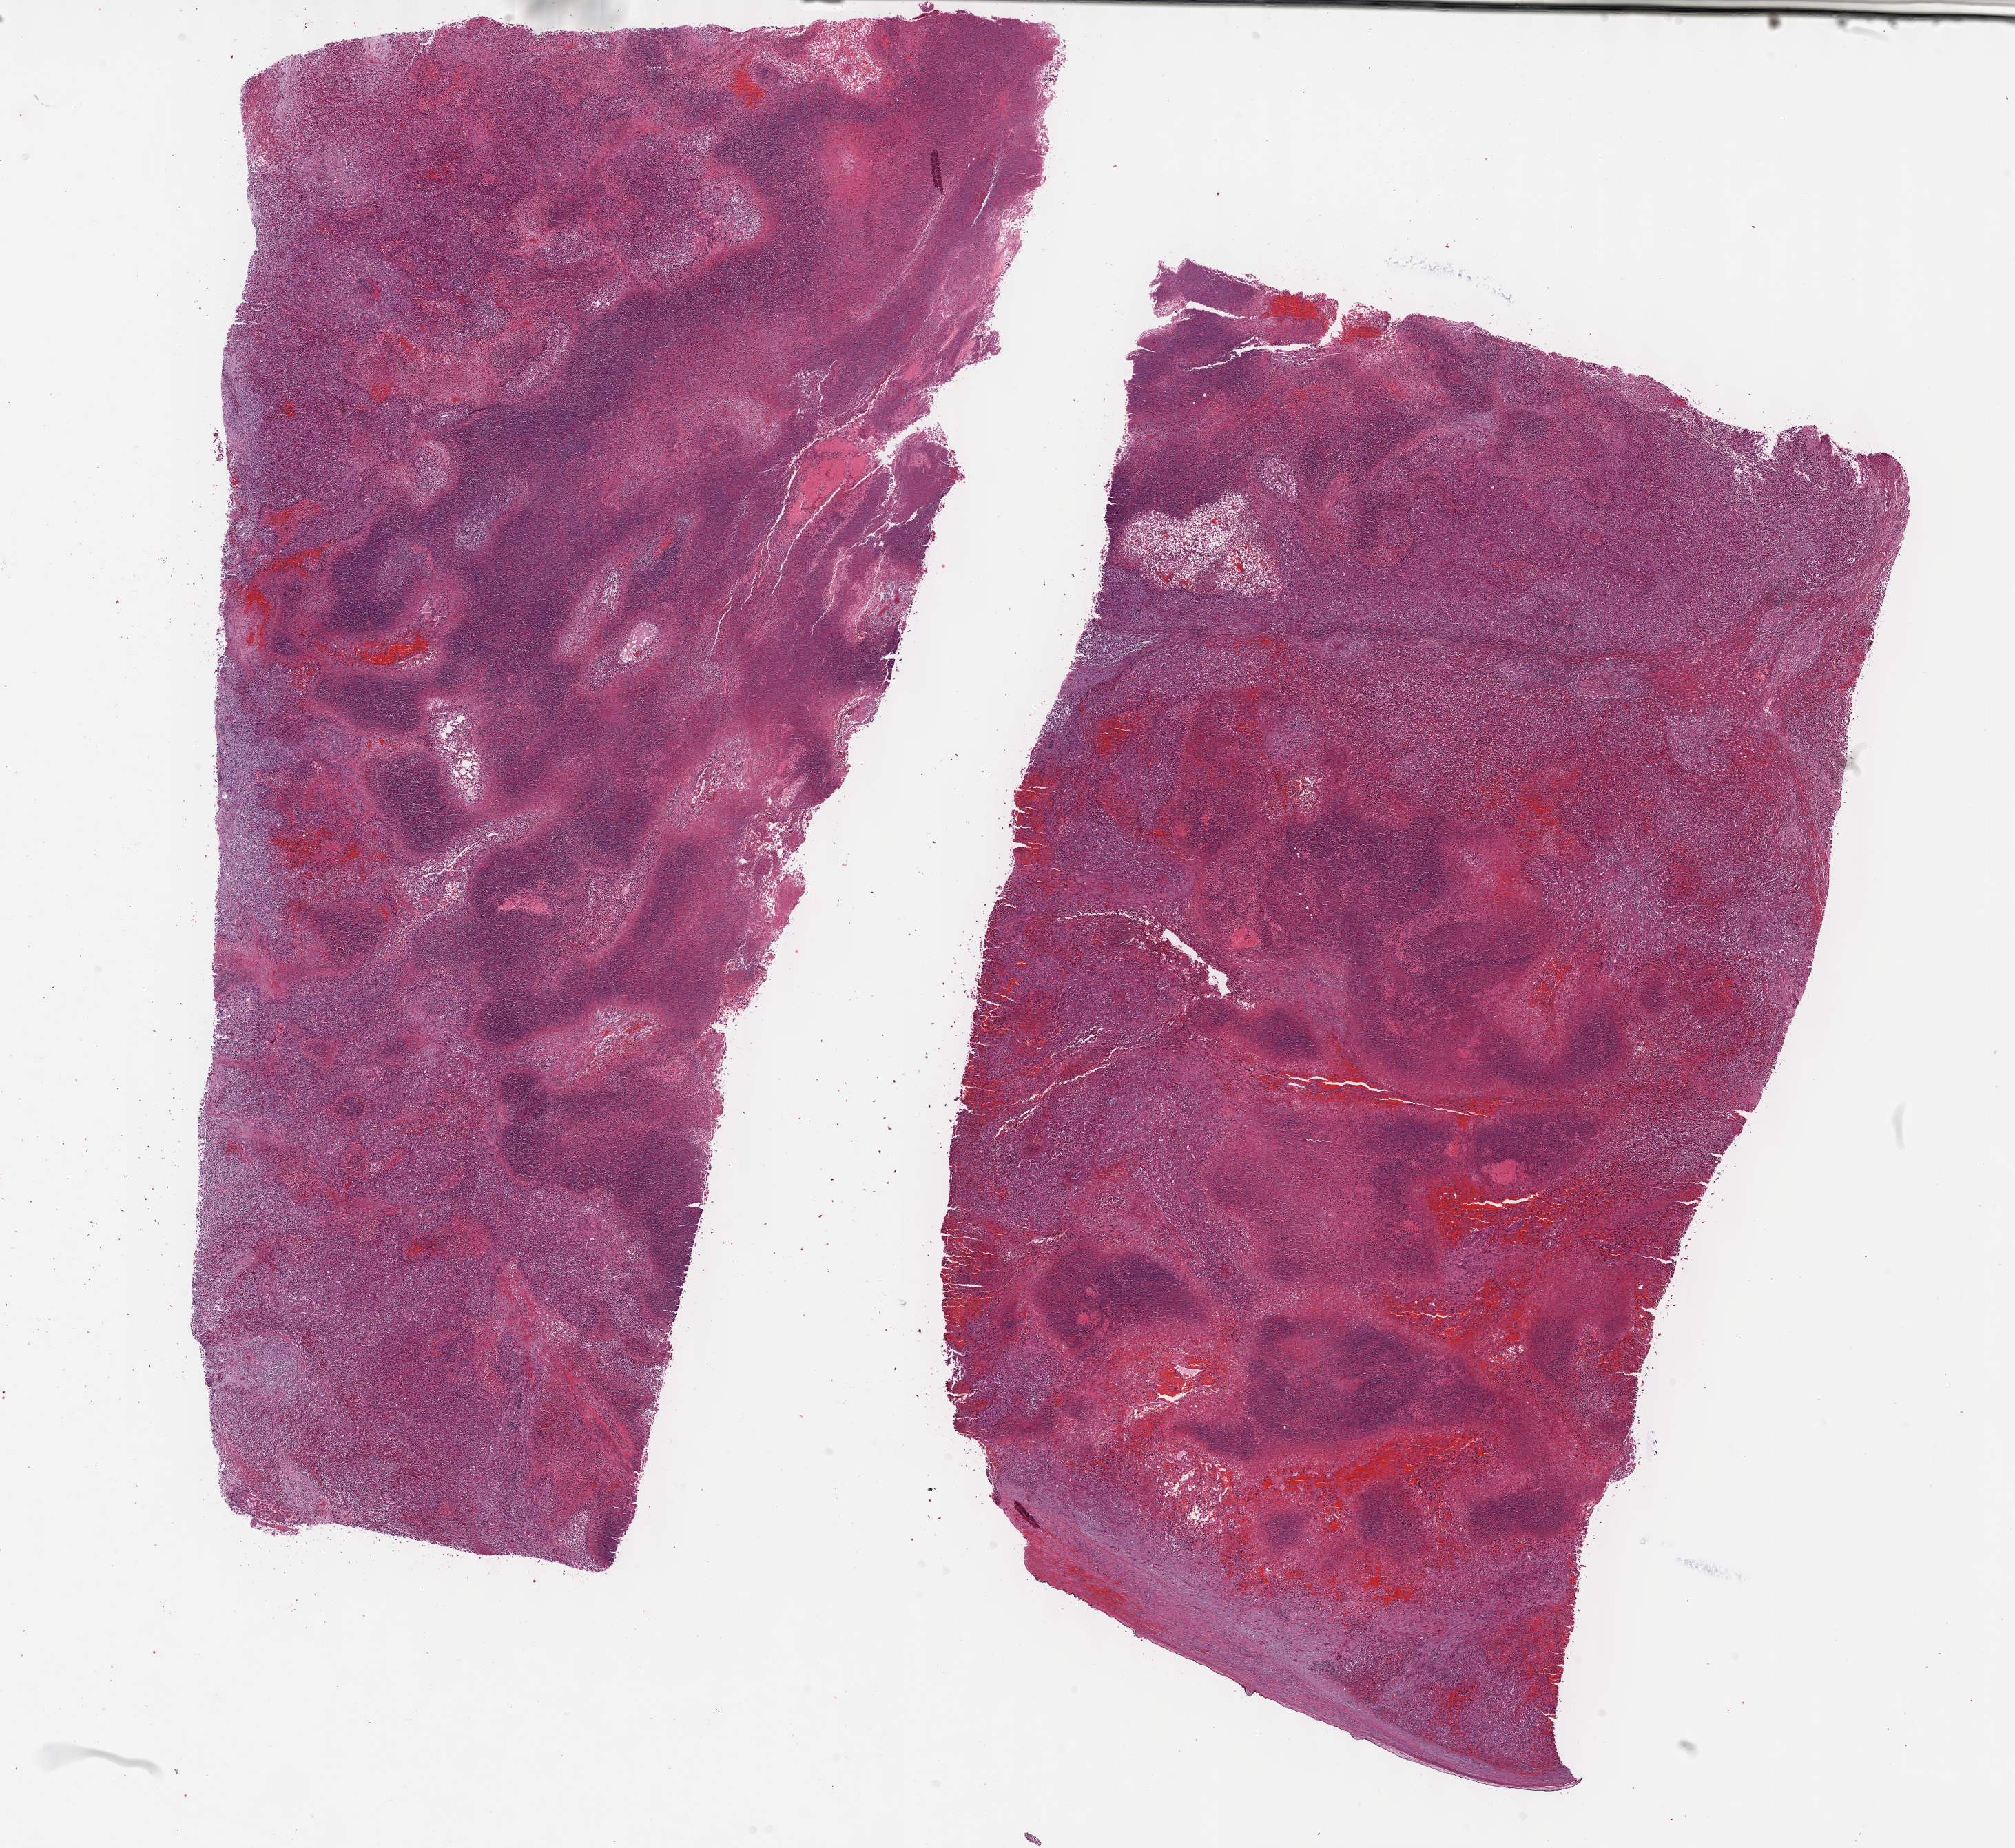
Whole-slide histology image, H&E-stained, shown as a low-resolution overview of the whole scanned area (about 23.7 x 21.7 mm). Formalin-fixed paraffin-embedded (FFPE) diagnostic section. Primary tumour sample from the bile duct. Male, age 52 years at initial diagnosis. Histologic grade: G3 (poorly differentiated).
Histologic diagnosis: Cholangiocarcinoma. AJCC pathologic stage: I.